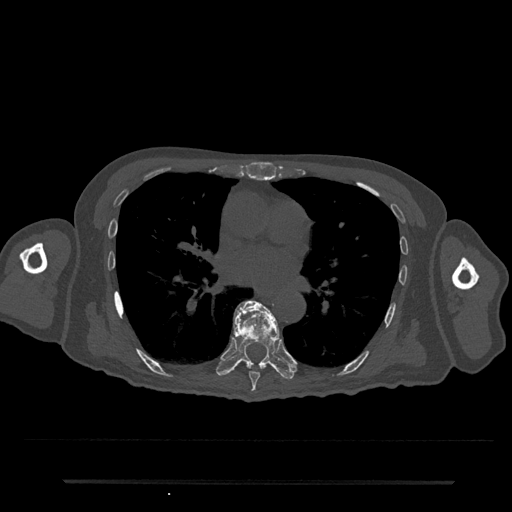
CT including the spine, one axial slice; reconstruction kernel Br40s/3; bone window (W 1800 / L 400 HU); 0.5 mm slice thickness; 512 × 512 image matrix, field of view 427 × 427 mm. Male patient, age 74 years. Case-level facts recorded for this patient, not image findings: primary cancer: prostate.
Structures marked on this image (semi-automatically segmented with operator editing):
- T7 vertebra: bounding box (x1, y1, x2, y2) in pixels: (234, 302, 267, 392)
- T8 vertebra: (216, 300, 295, 380)